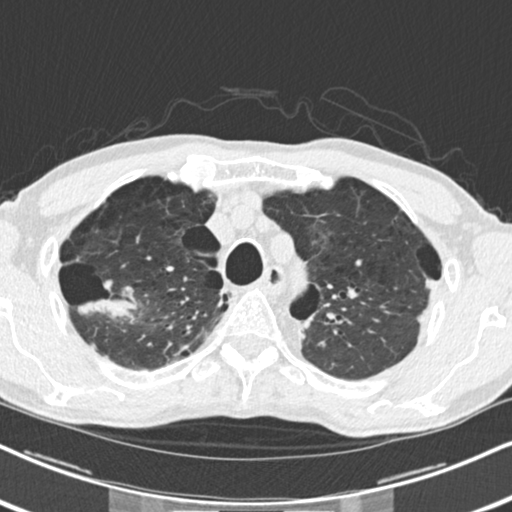
Axial slice from a low-dose chest CT screening exam. First (baseline) screen. Lung window (W 1500 / L -600 HU). 2 mm slice thickness. 120 kVp. Slice 50 of 250 in the series. 512 × 512 image matrix, field of view 325 × 325 mm. Male, age 71 years at enrolment.
- Expert-annotated lung lesion, bounding box (x1, y1, x2, y2) in pixels: (91, 265, 150, 317).
- The screening reader recorded 2 non-calcified nodules or masses ≥4 mm on this exam (right upper lobe, left upper lobe); which of them this box marks is not recorded.
- Later outcome: lung cancer diagnosed 454 days after this screen (after the second annual screen) — adenocarcinoma, NOS, right upper lobe, well differentiated (G1), stage IA (AJCC 6th edition), 30 mm at pathology.